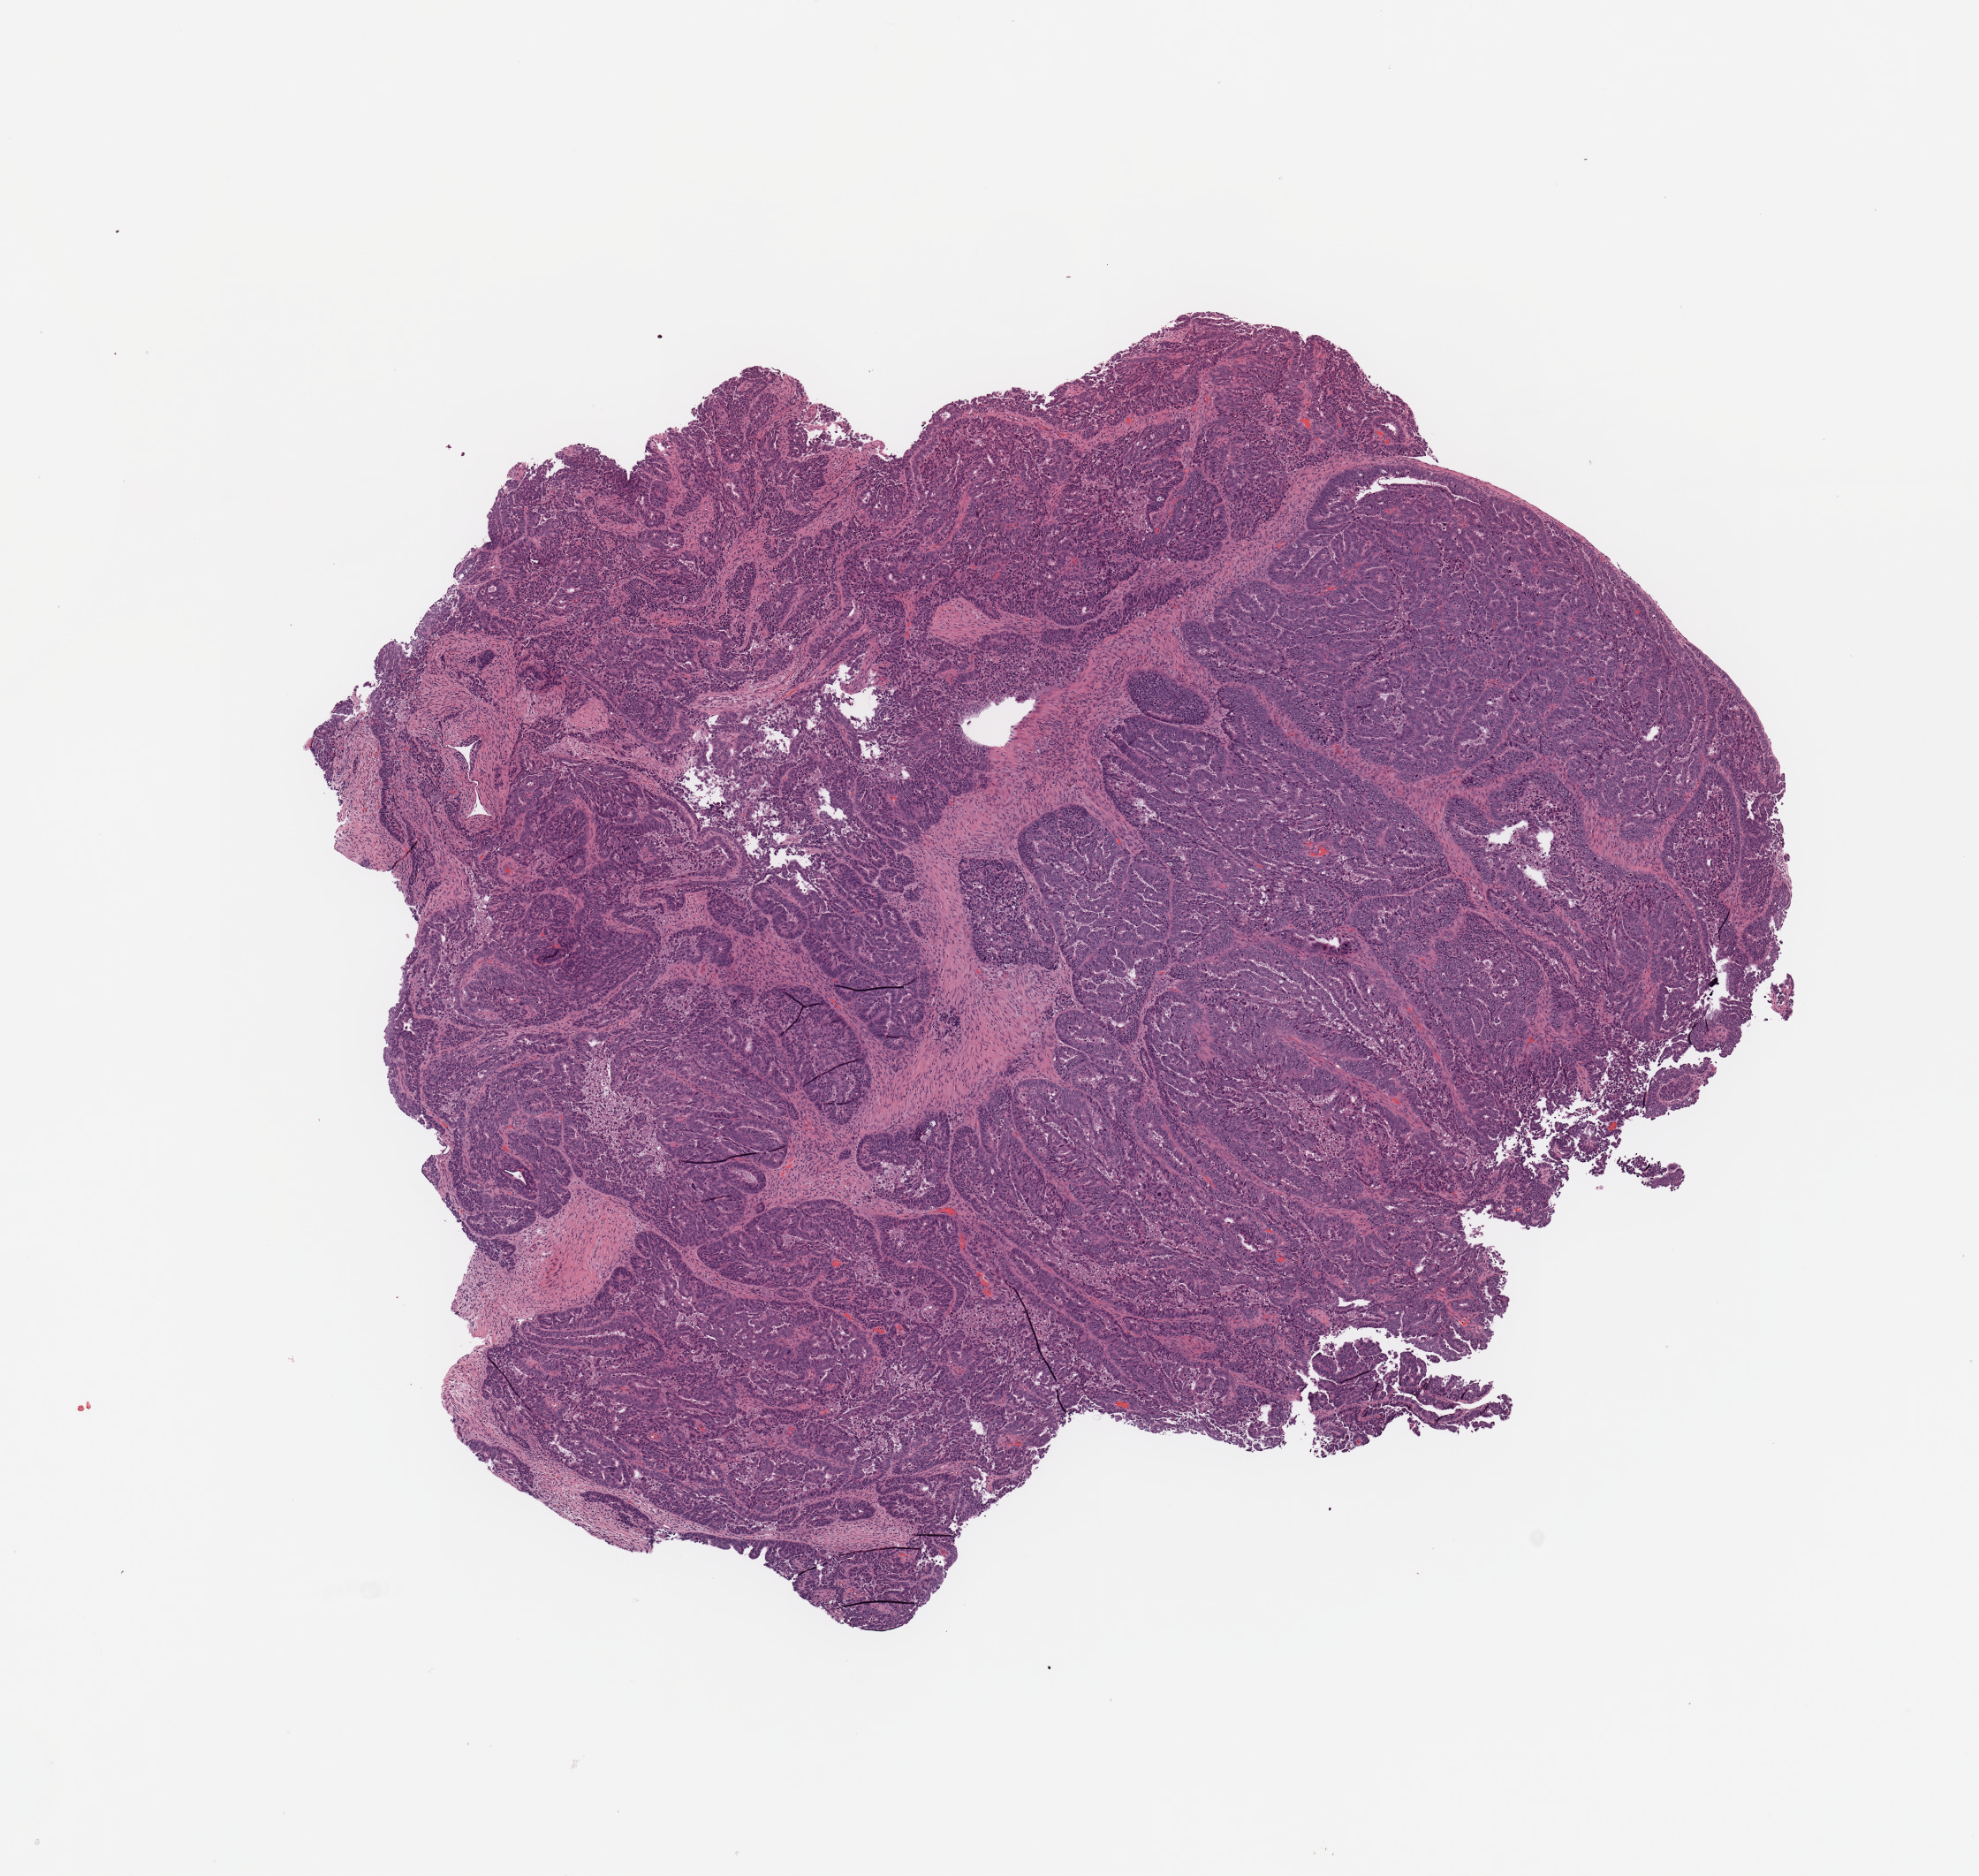
H&E-stained whole-slide image, shown as a low-resolution overview of the whole scanned area (about 8.9 x 8.4 mm). Tumour tissue sample, uterus. Female, 67 y/o. Histologic grade: G3 (poorly differentiated).
Histologic diagnosis: Endometrioid adenocarcinoma, NOS. AJCC pathologic stage: IB.